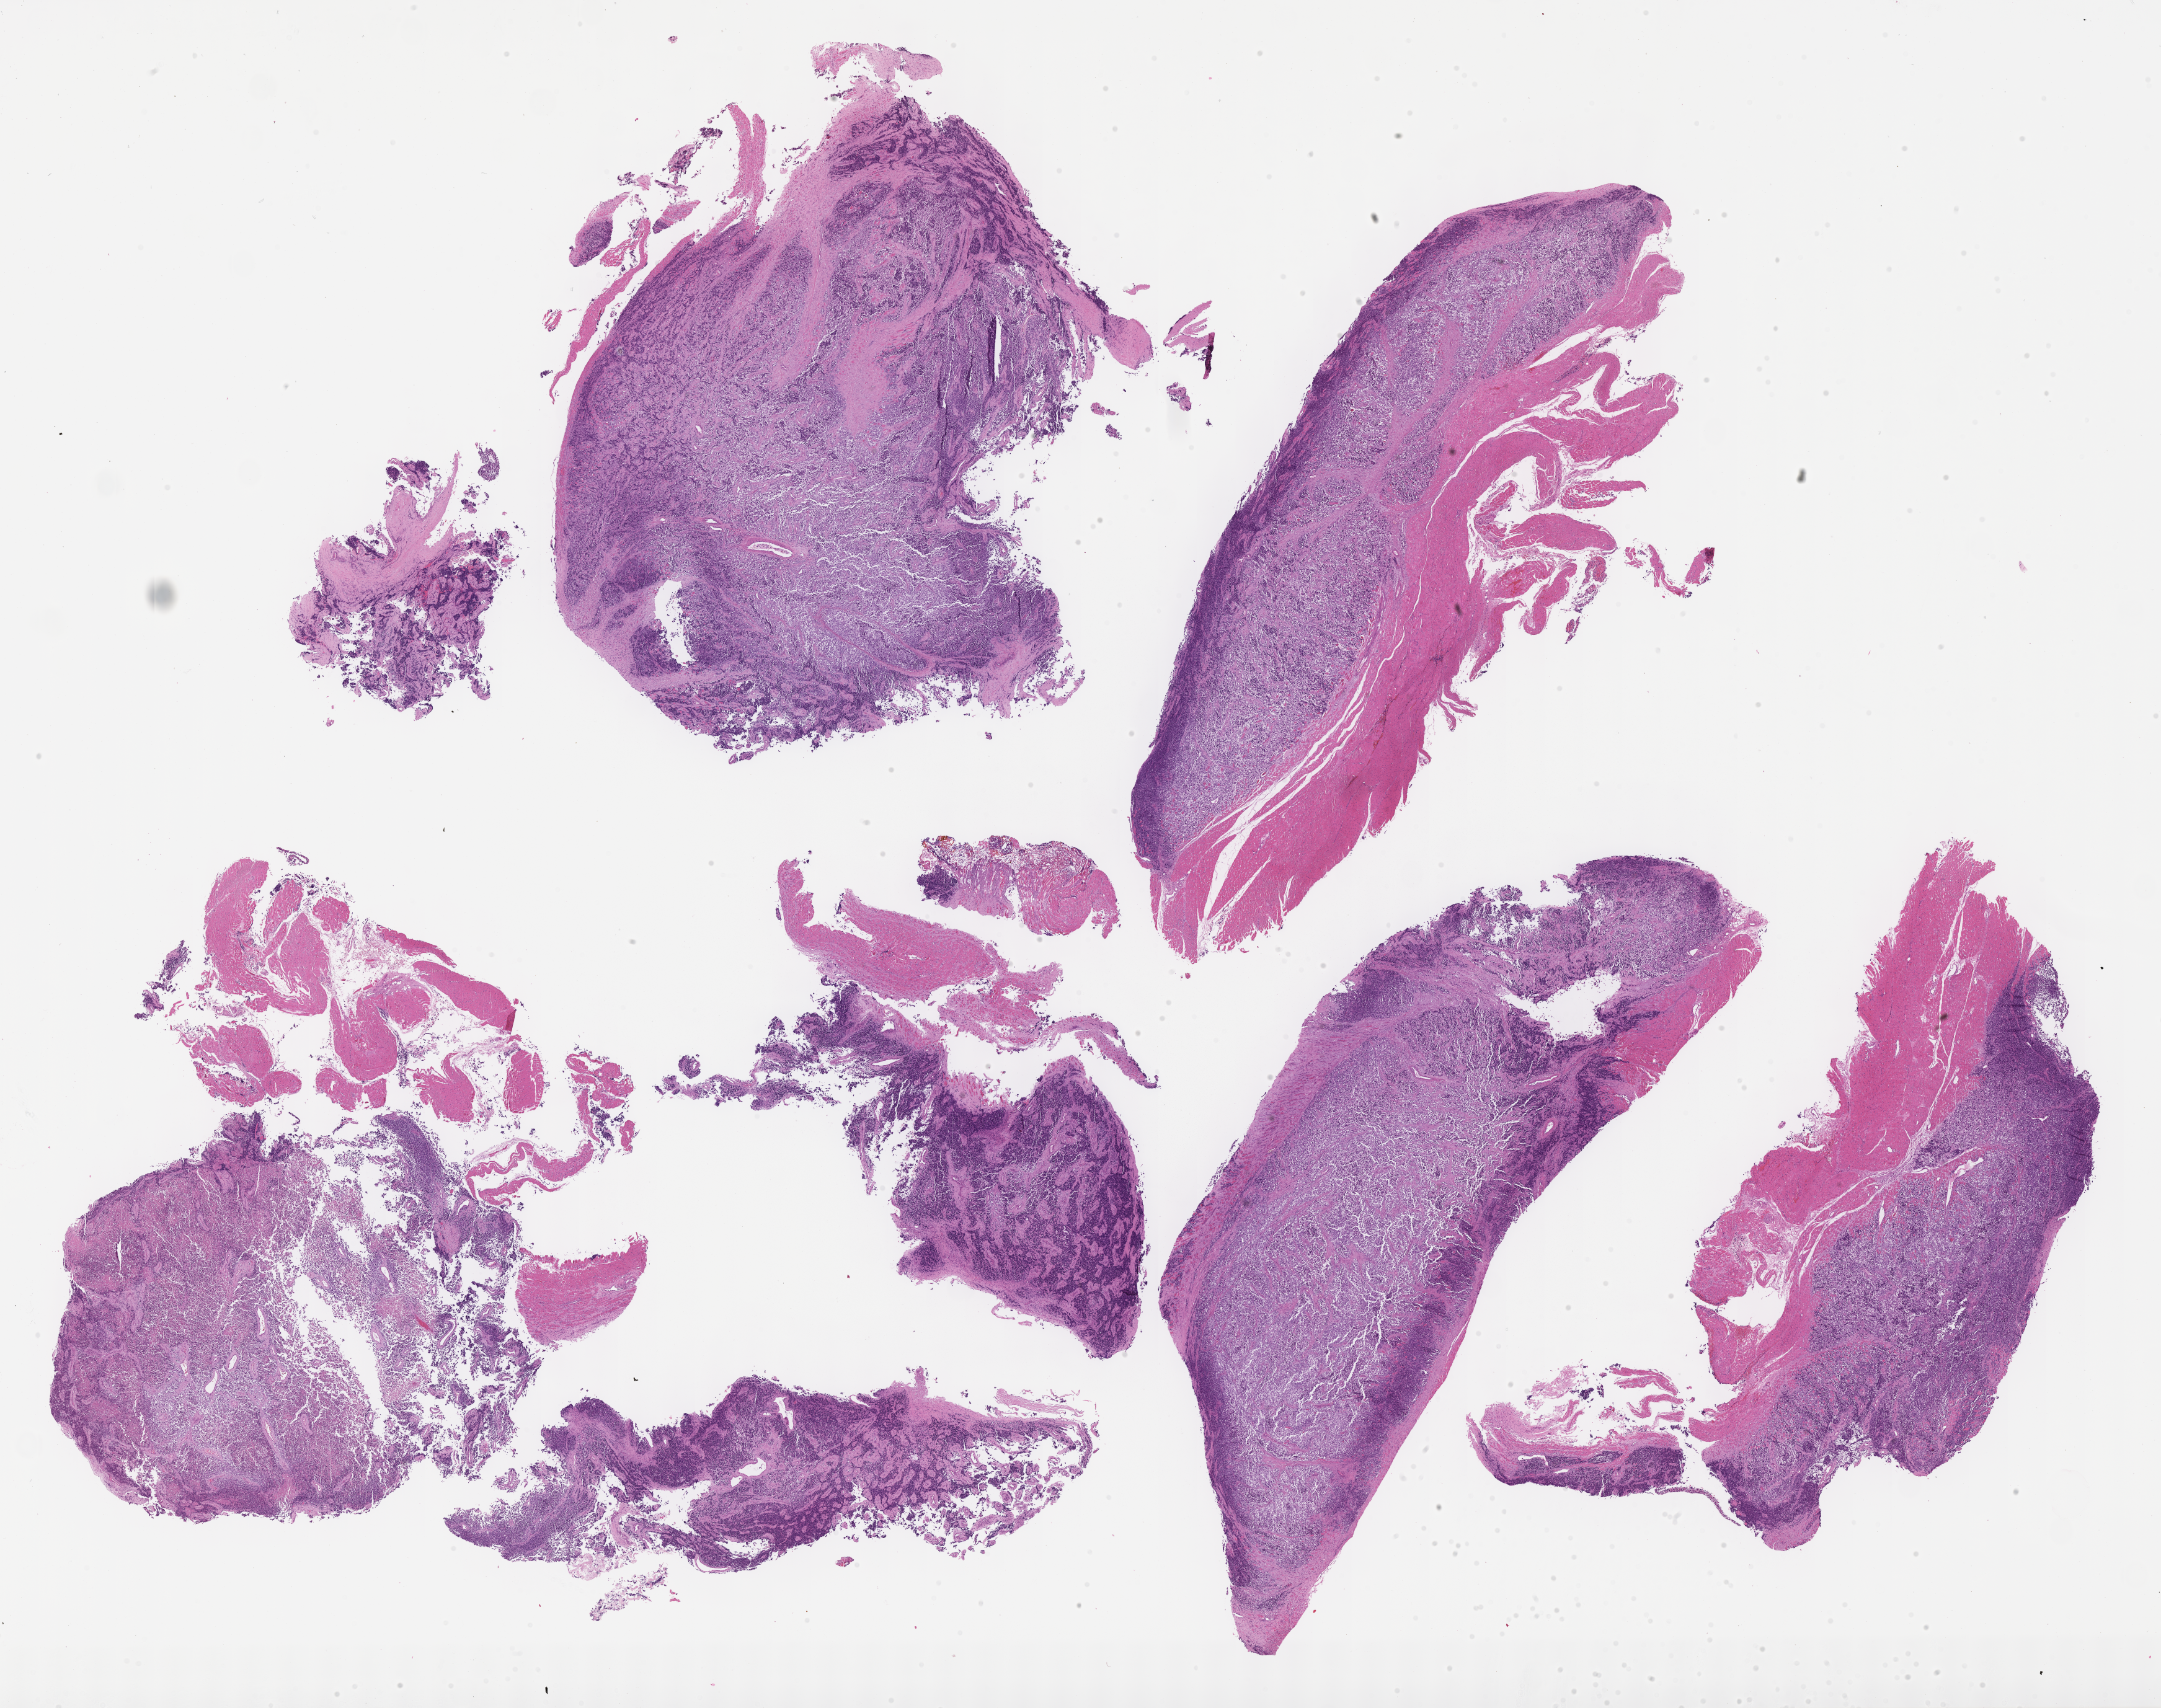
Hematoxylin and eosin (H&E) whole-slide image of tumor tissue — whole scanned area (about 28.2 x 22.3 mm) shown as a low-resolution overview, formalin-fixed, paraffin-embedded (FFPE) tissue, site: paraspinal, posterior. Female patient, age at diagnosis 4.3 years.
Stage (as recorded): 4. Metastatic status at presentation (as recorded): metastatic. Diagnosis: rhabdomyosarcoma; histological classification: alveolar rhabdomyosarcoma.